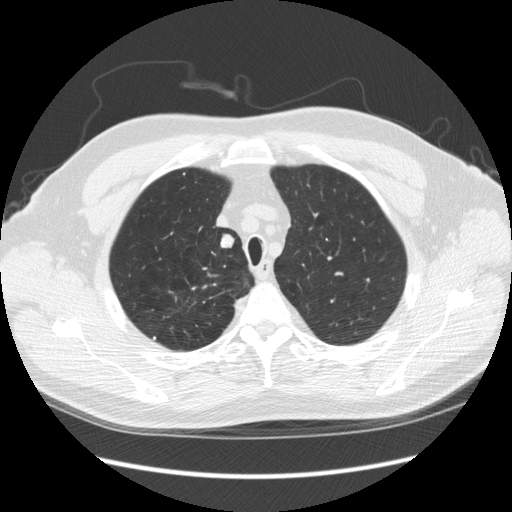
Chest CT (low-dose screening protocol), one axial image. Third annual screen. Lung window (W 1500 / L -600 HU). 2.5 mm slice thickness. Standard (soft-tissue) reconstruction kernel (STANDARD). Slice 40 of 248 in the series. Male participant, aged 64 years at enrolment. Former smoker at enrolment.
- Lesion marked by an expert reader, bounding box <199,230,242,262> (left, top, right, bottom; pixels).
- The screening reader recorded 4 non-calcified nodules or masses ≥4 mm on this exam (right upper lobe, right upper lobe, right upper lobe, right upper lobe); which of them this box marks is not recorded.
- Lung cancer was diagnosed 15 days after this screen: adenocarcinoma, NOS, right upper lobe, moderately differentiated (G2), stage IA (AJCC 6th edition), 14 mm at pathology.